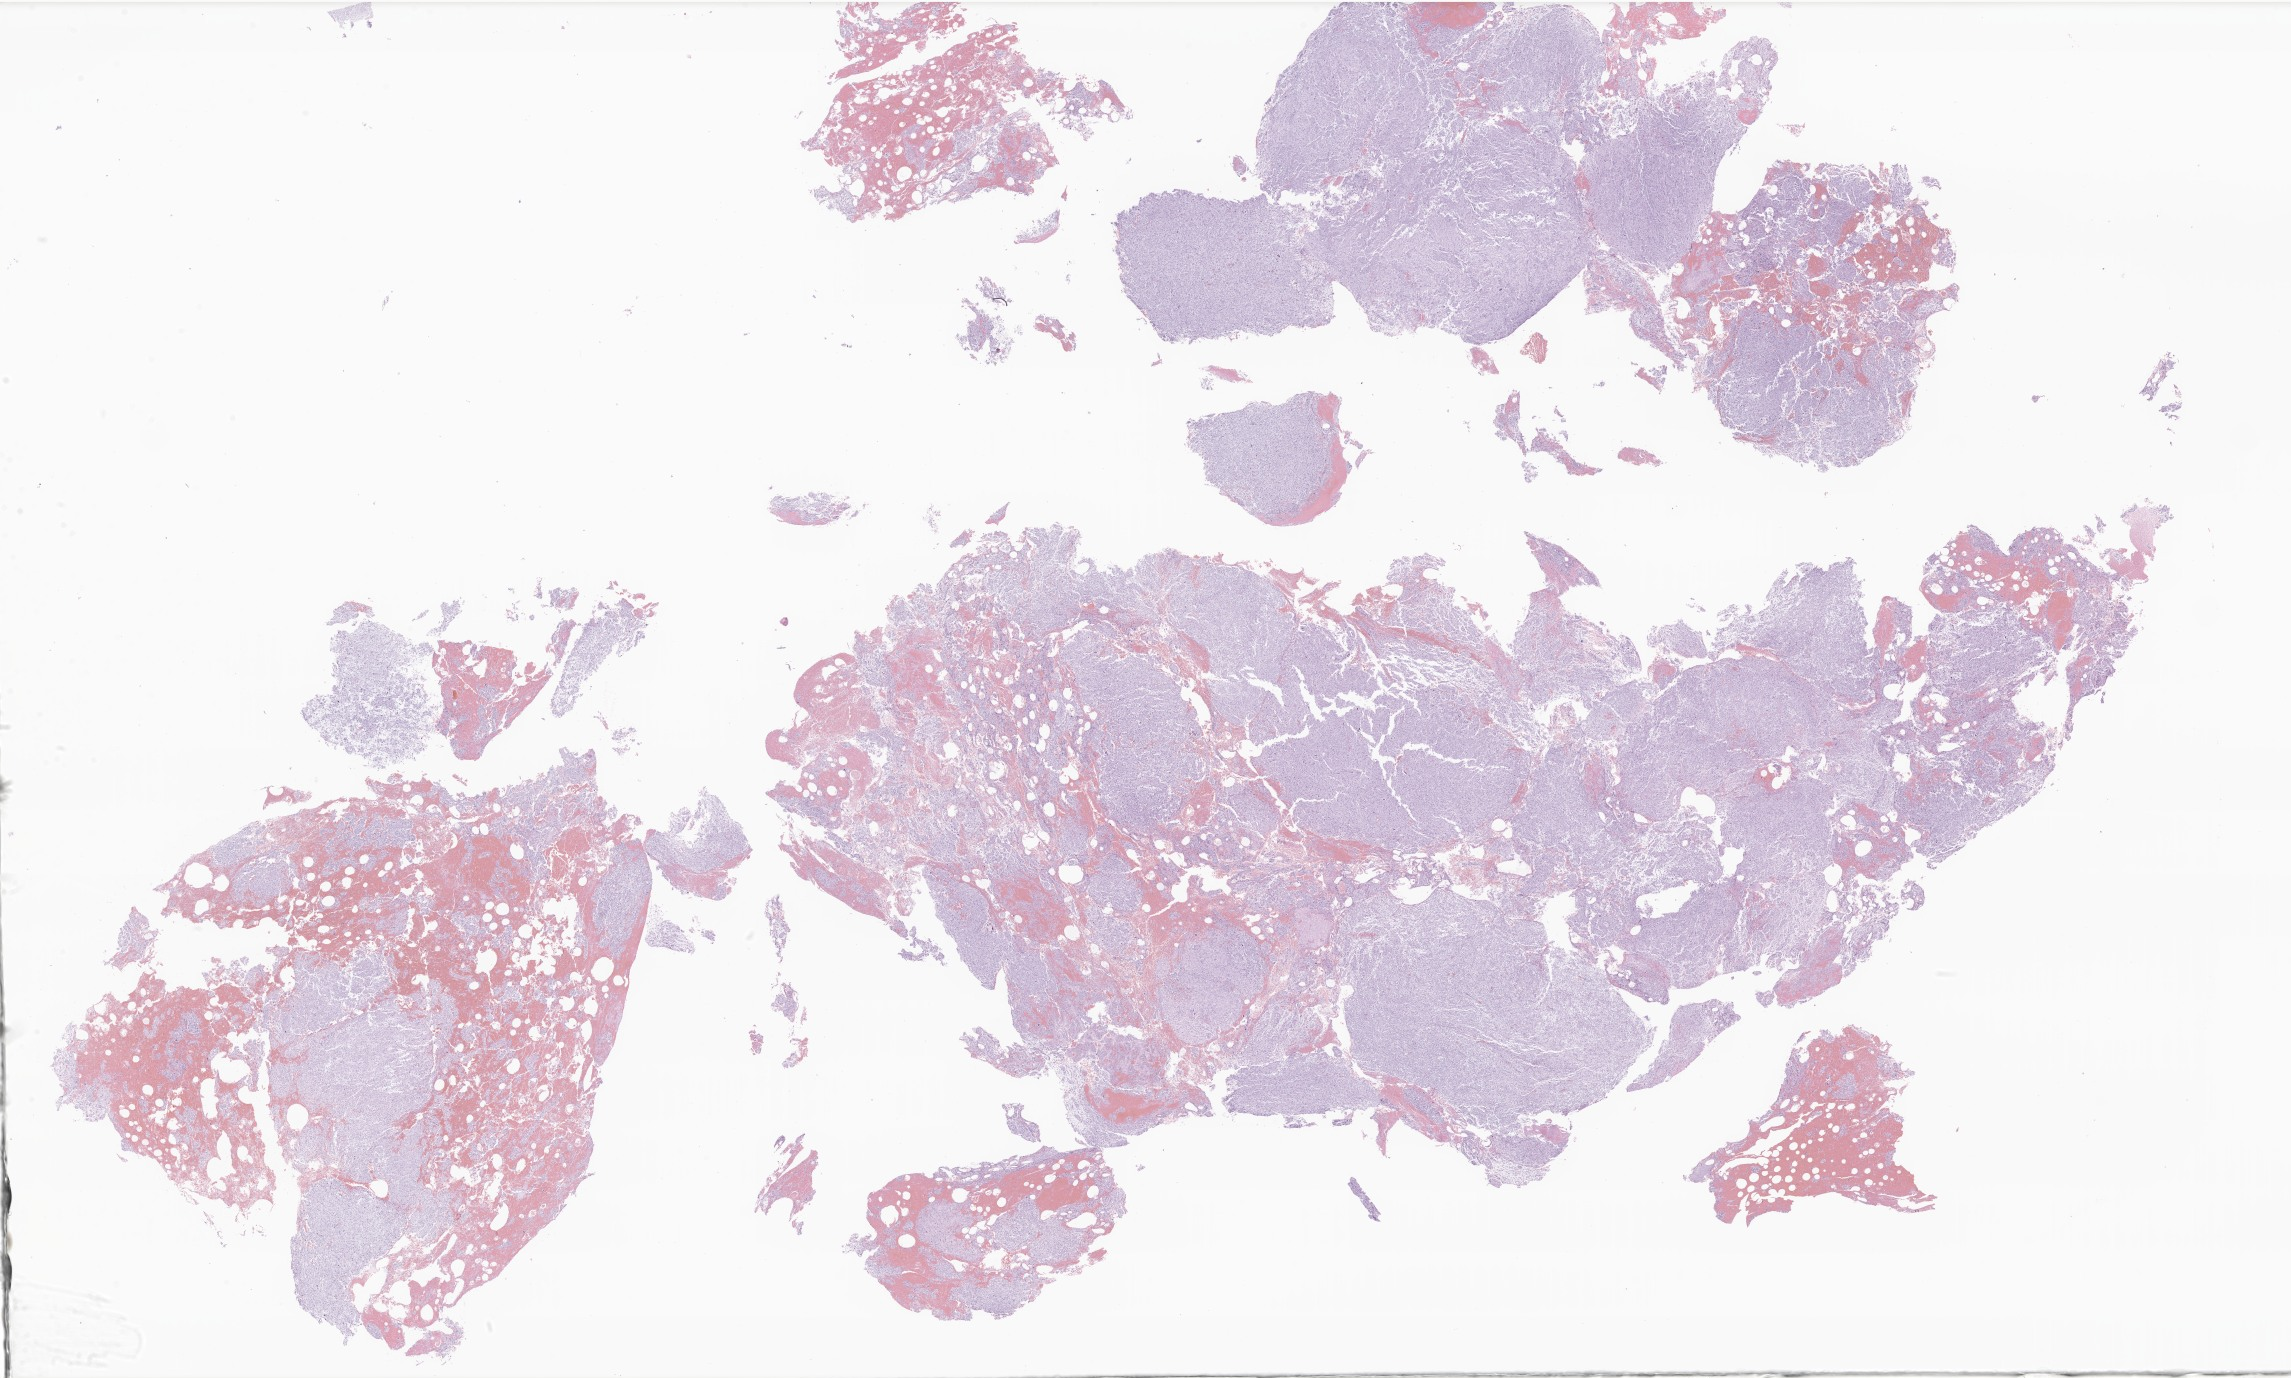
Hematoxylin and eosin (H&E) whole-slide image of tumor tissue from the brain, a low-resolution overview of the entire scanned area, about 38.6 x 23.2 mm. FFPE section. Patient: male, age 92 months (7 years 8 months).
Diagnosis: Glioma, malignant.